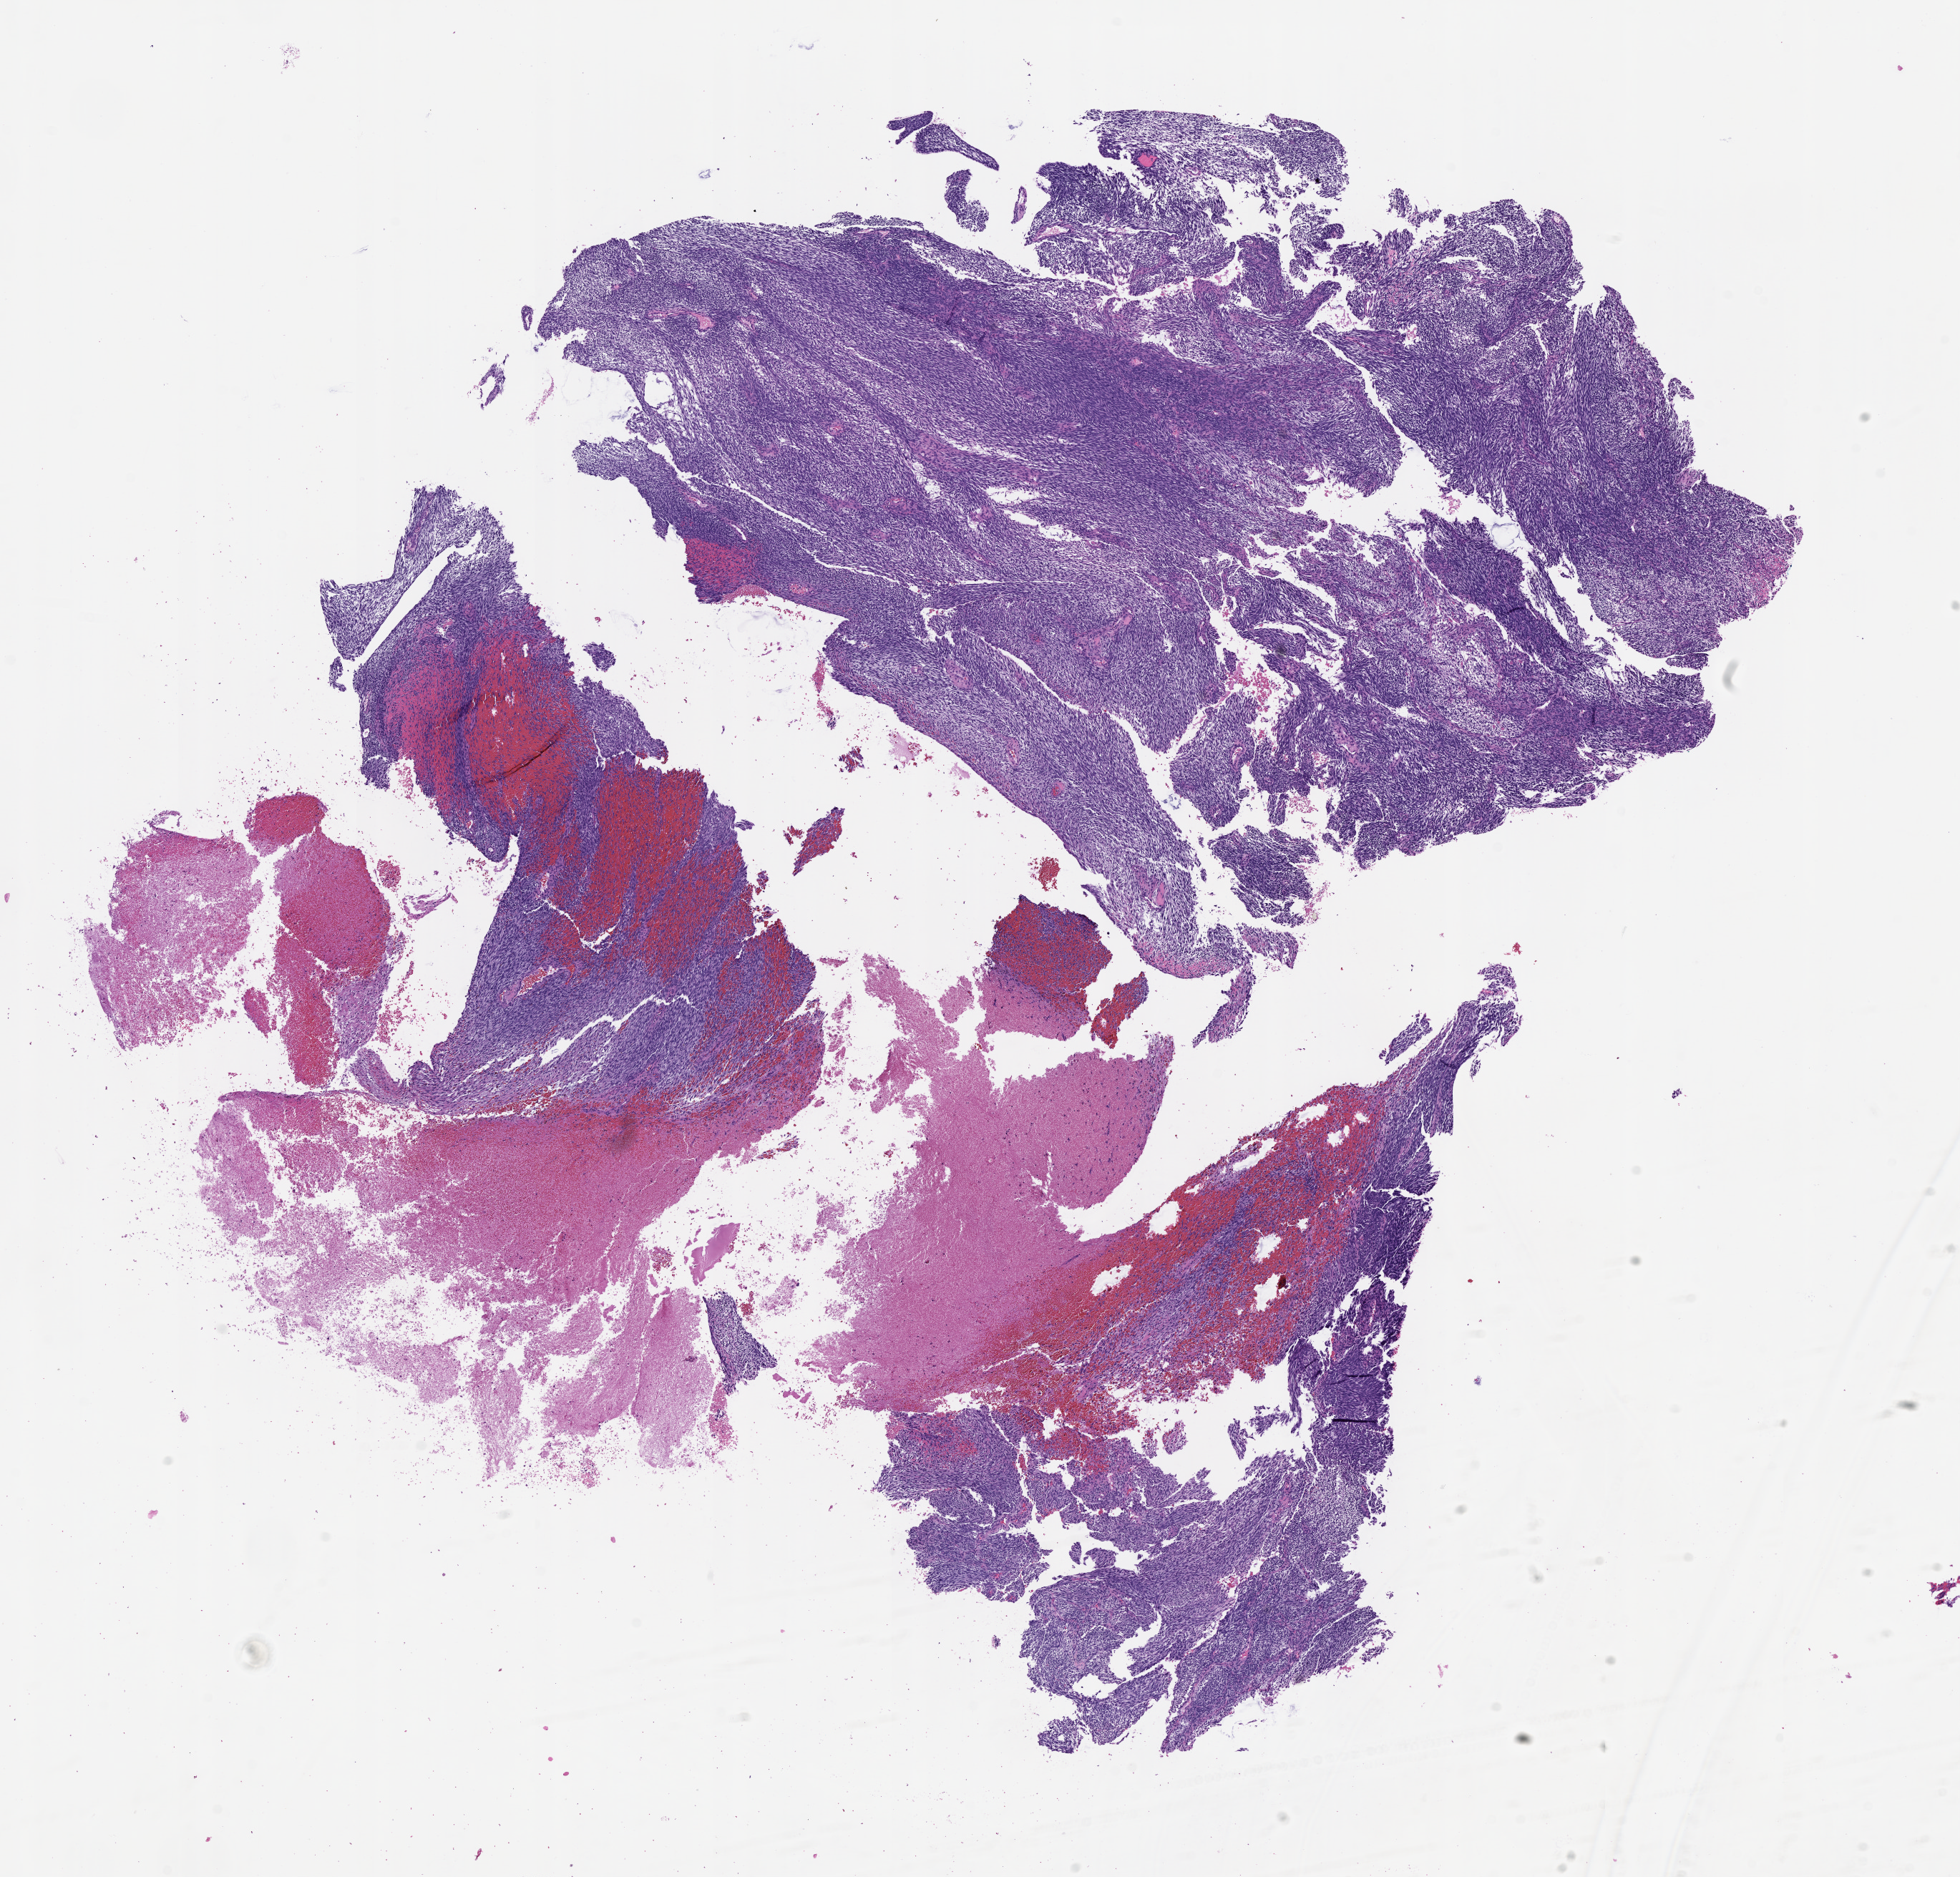
H&E whole-slide image, a low-resolution overview of the entire scanned area, about 11.0 x 10.6 mm (from a 20x scan).
Patient diagnosis (cohort enrolment): sarcoma (site not recorded at cohort level).